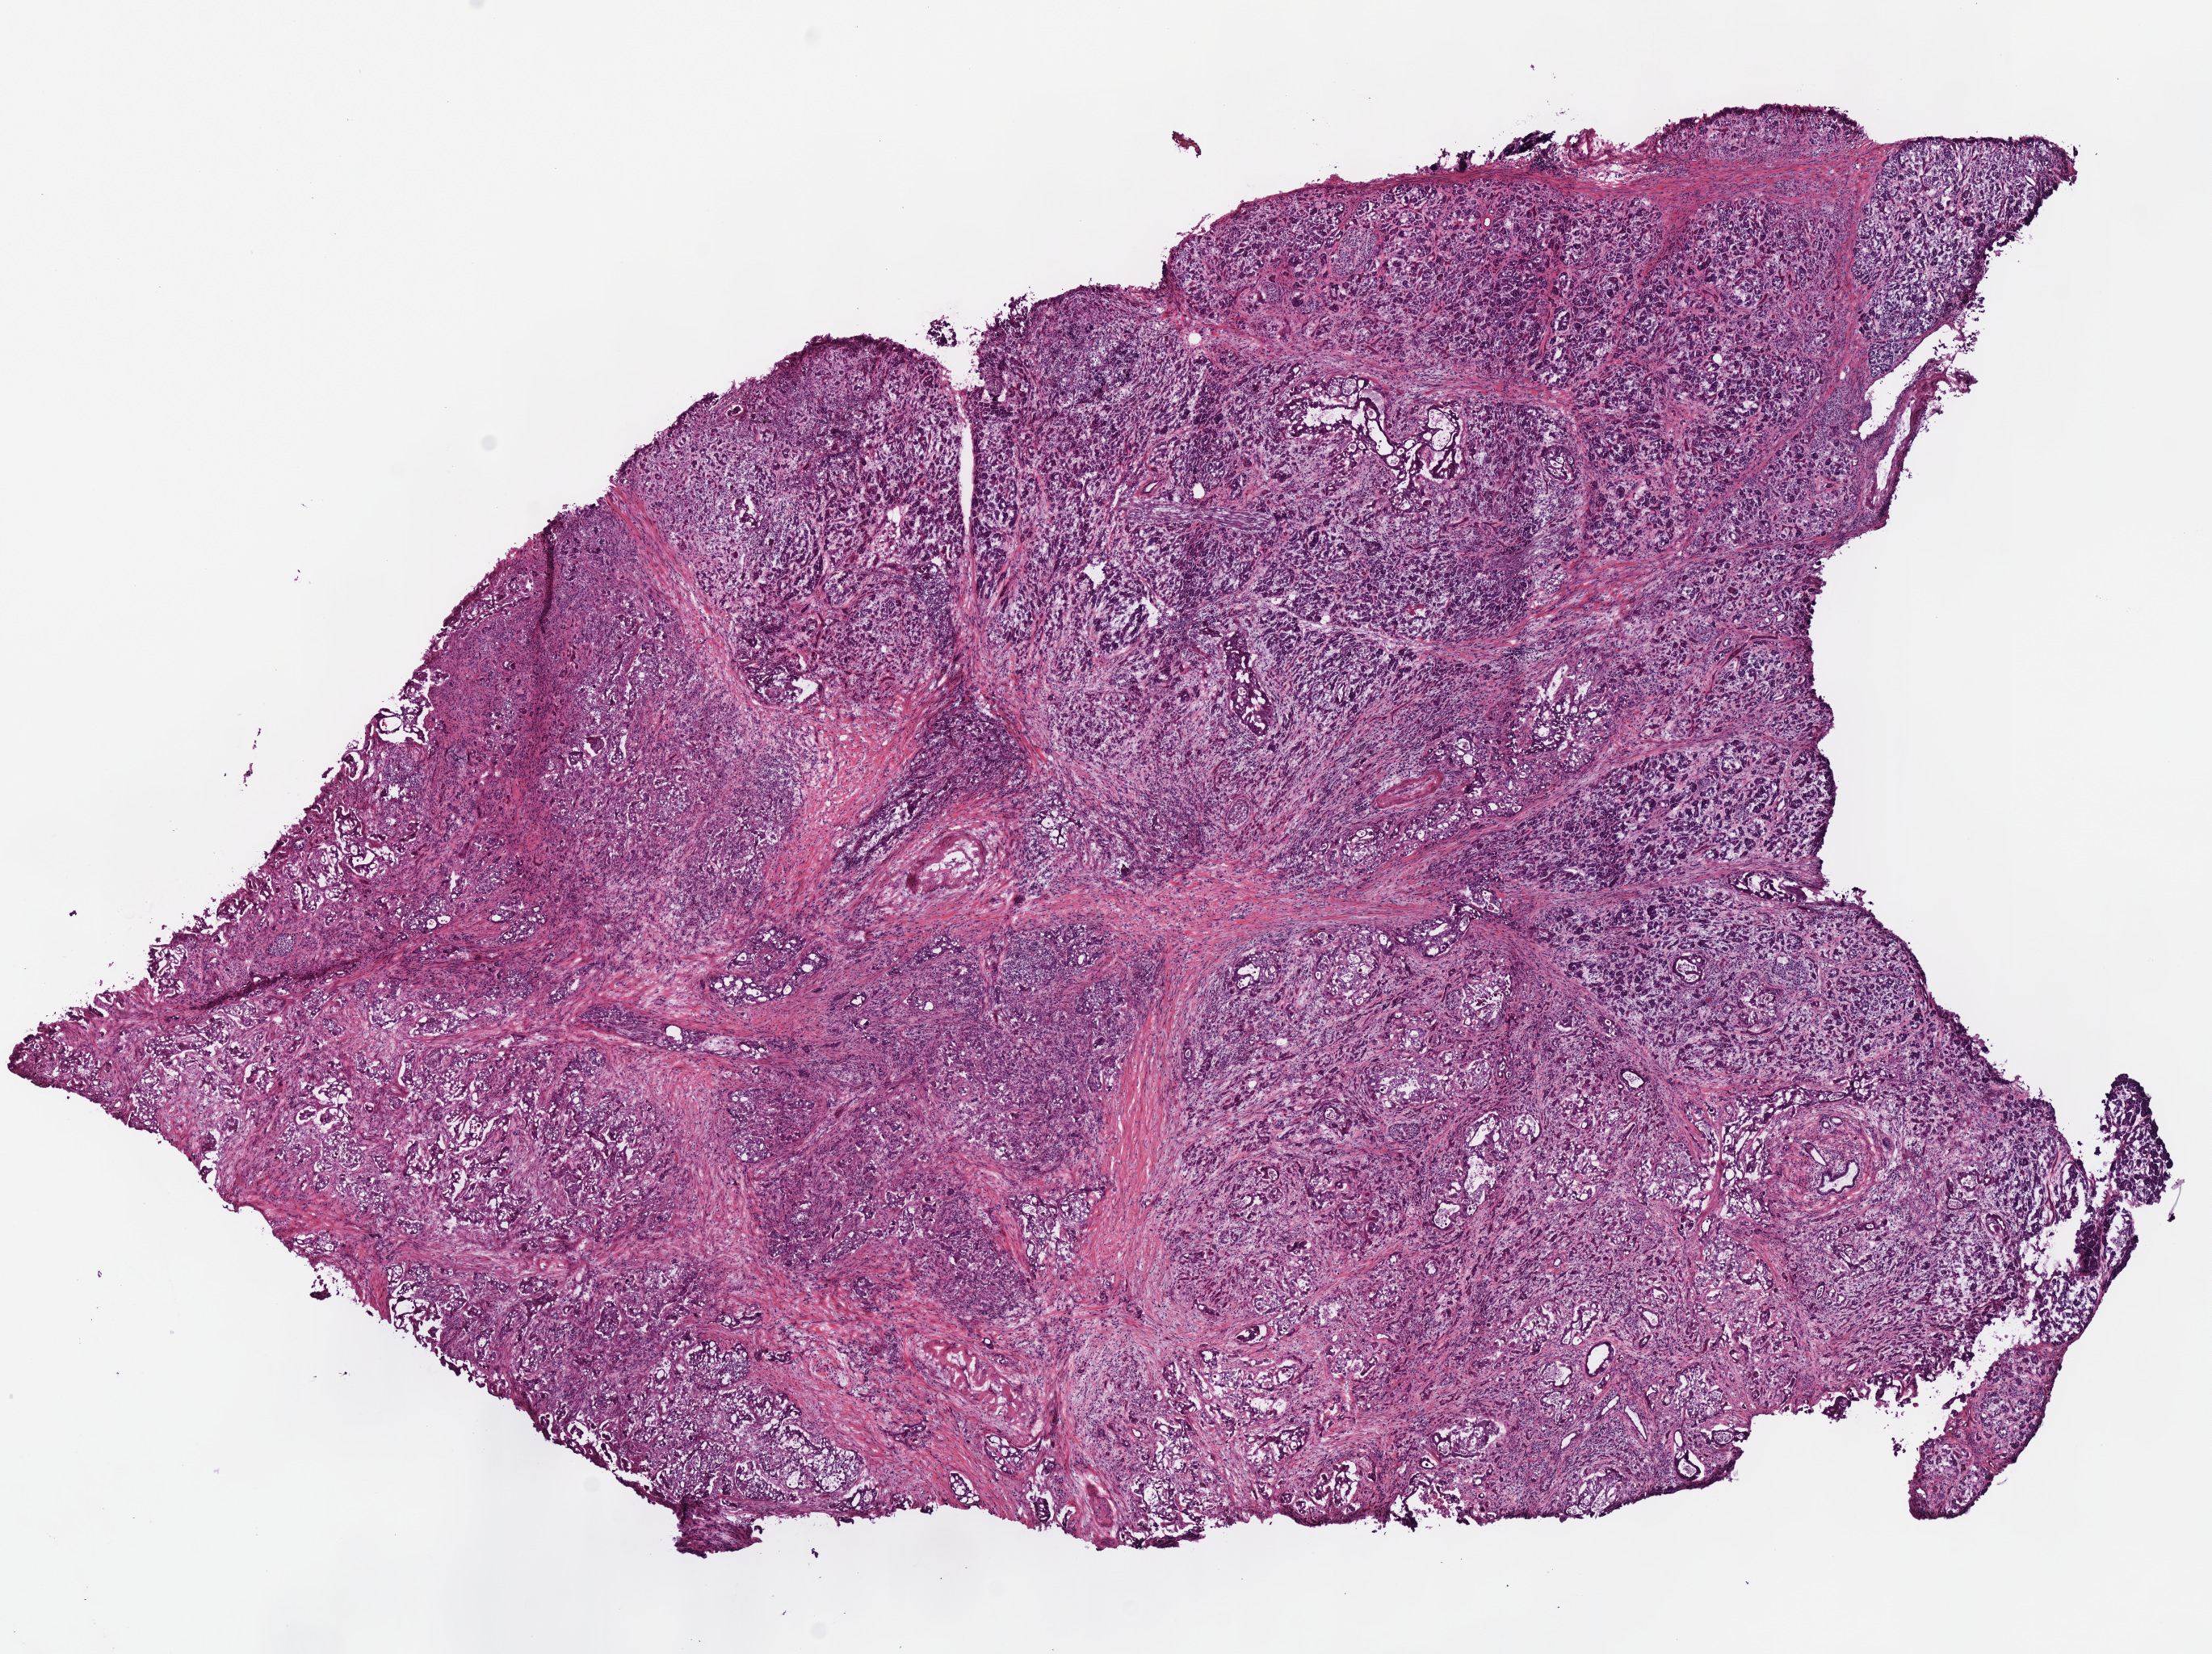
Hematoxylin and eosin (H&E) stained whole-slide image — a low-resolution overview of the entire scanned area, about 10.8 x 8.1 mm; frozen section; primary tumour sample from the pancreas. Female, age 64 years at initial diagnosis.
Pathologic diagnosis: Infiltrating duct carcinoma, NOS (head of pancreas).